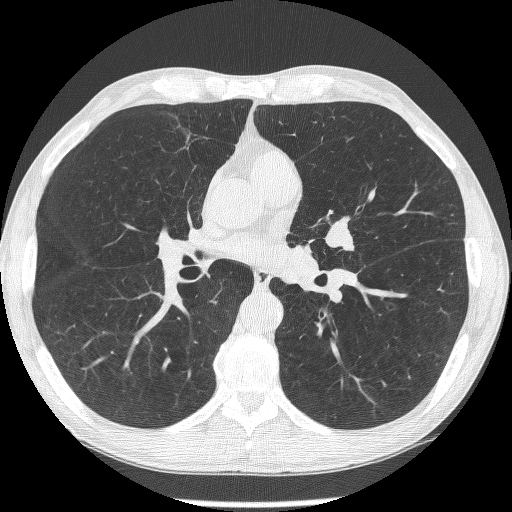
Chest CT (low-dose screening protocol), one axial image; second screening round (one year after baseline); lung window (W 1500 / L -600 HU); 1.25 mm slice thickness; 120 kVp; slice 143 of 293 in the series; 512 × 512 image matrix, field of view 326 × 326 mm. Male, age 62 years at enrolment. Former smoker at enrolment.
Lesion marked by an expert reader, bounding box <318,217,368,265> (left, top, right, bottom; pixels). The screening reader recorded 2 non-calcified nodules or masses ≥4 mm on this exam; which of them this box marks is not recorded.